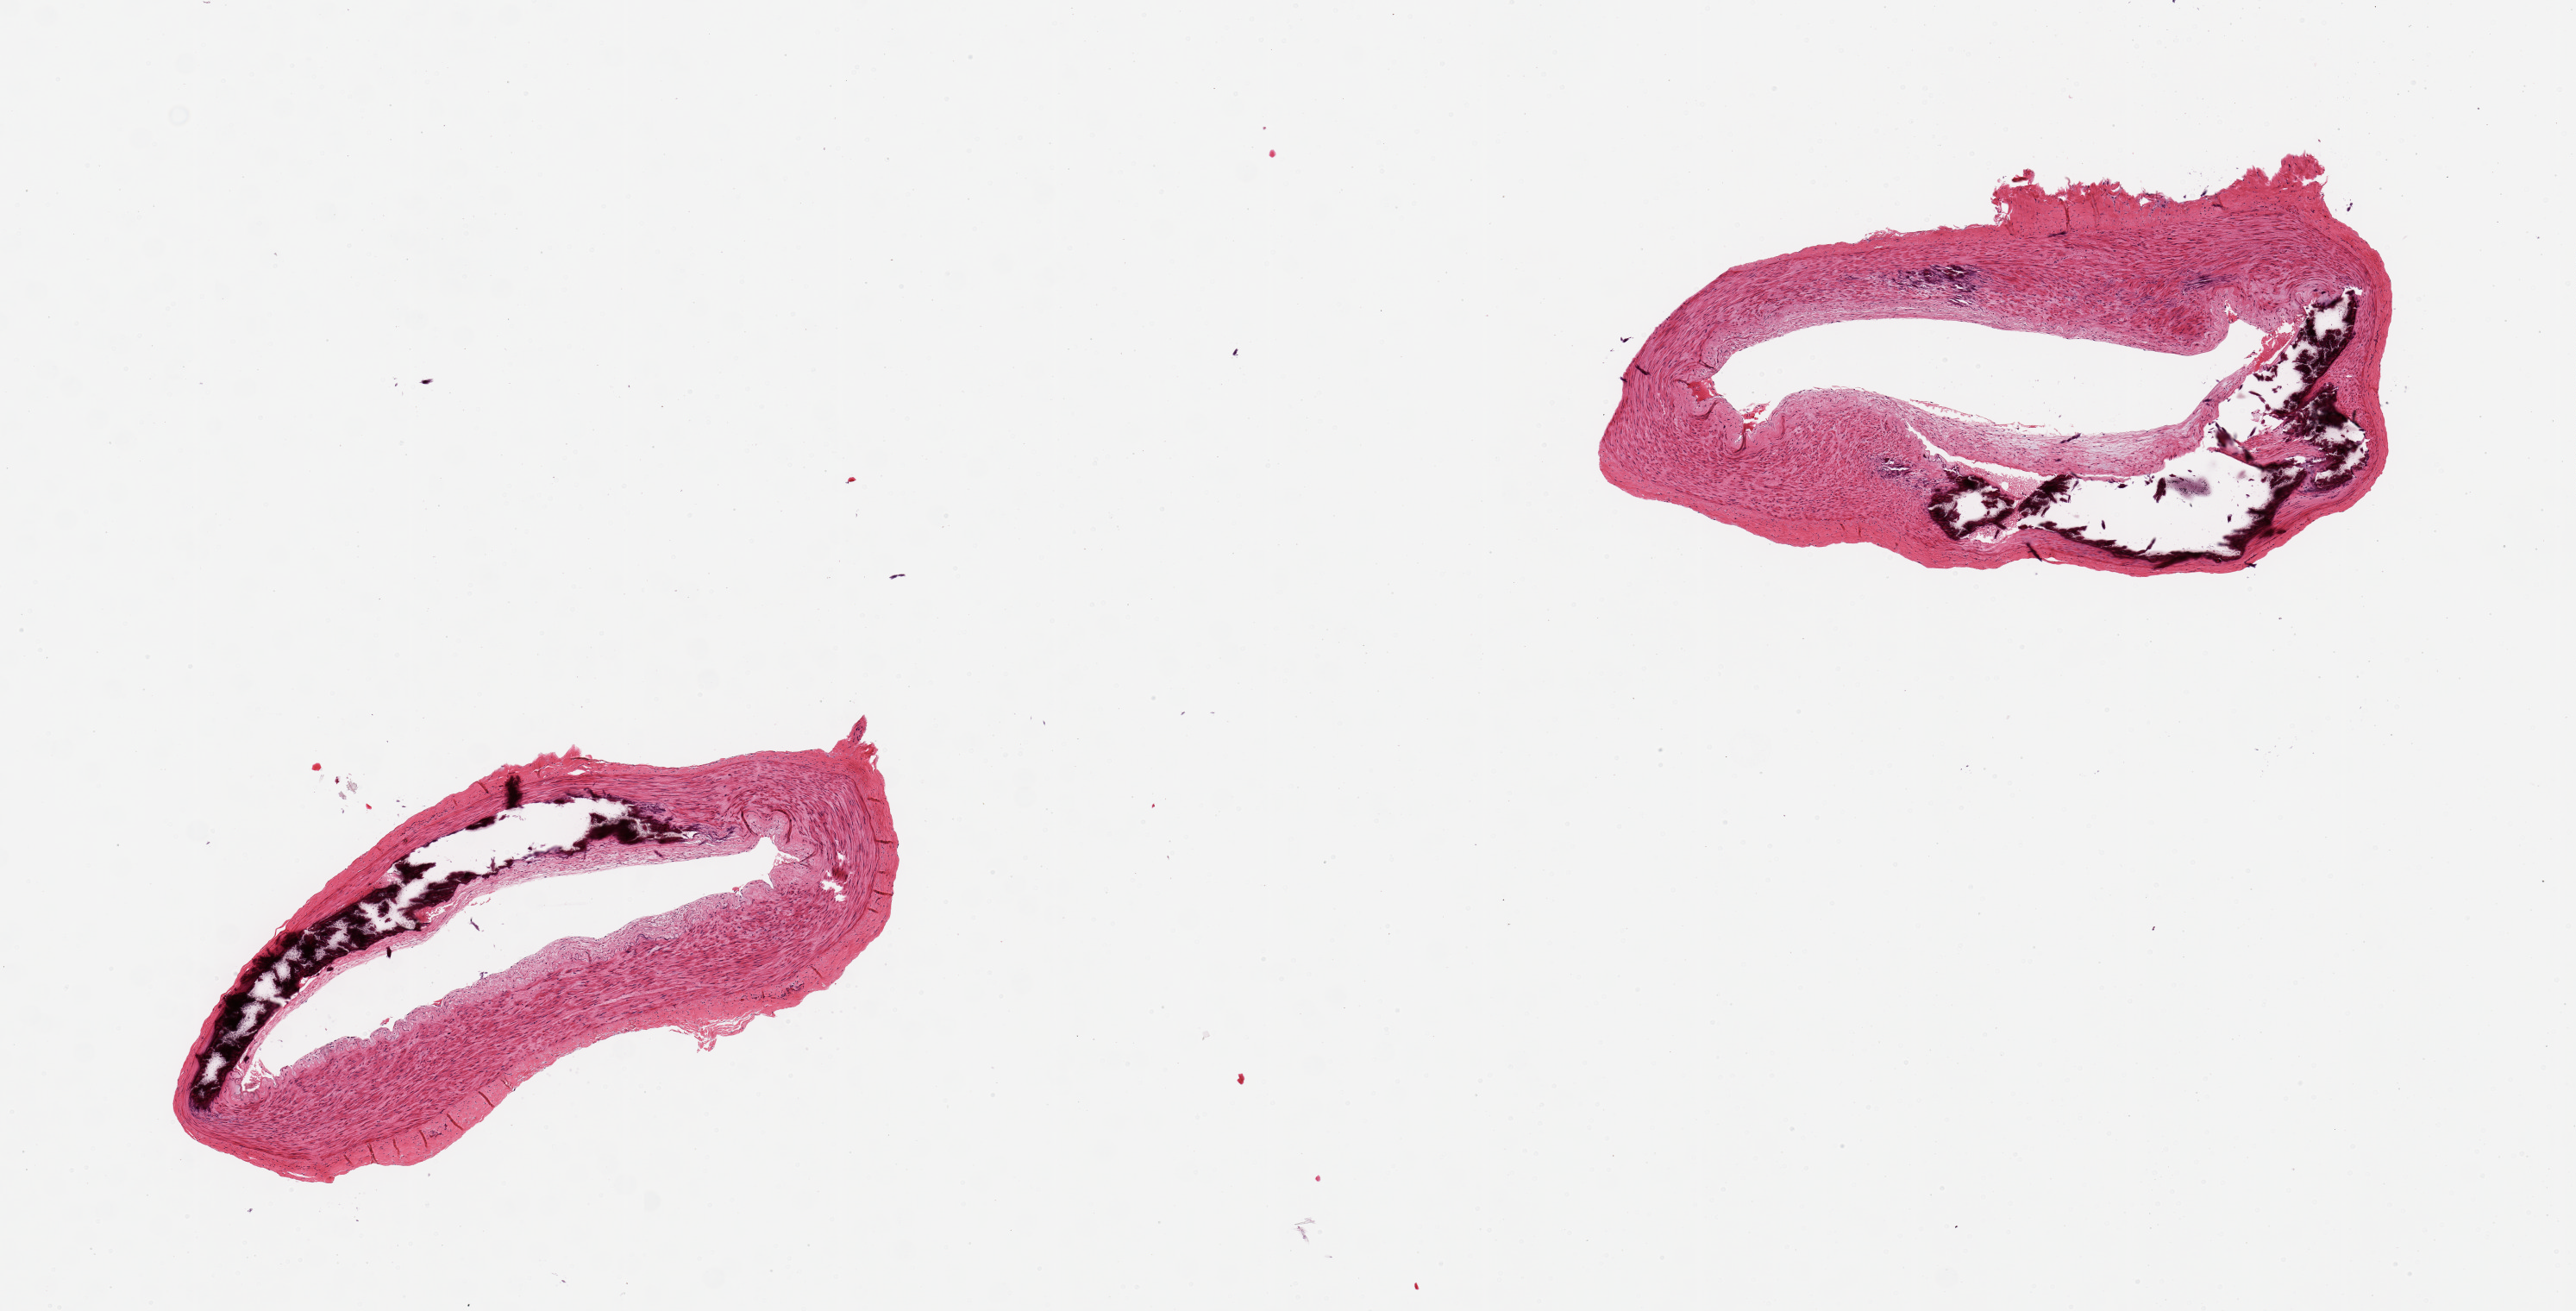
H&E whole-slide image — shown as a low-resolution overview of the whole scanned area (about 11.8 x 6.0 mm), PAXgene-fixed paraffin-embedded (PFPE) section, section of tibial artery (target tissue), tissue donor sample.
Reviewer comment on this tissue sample: 2 pieces, Monckeberg's medial sclerosis/calcifications present.